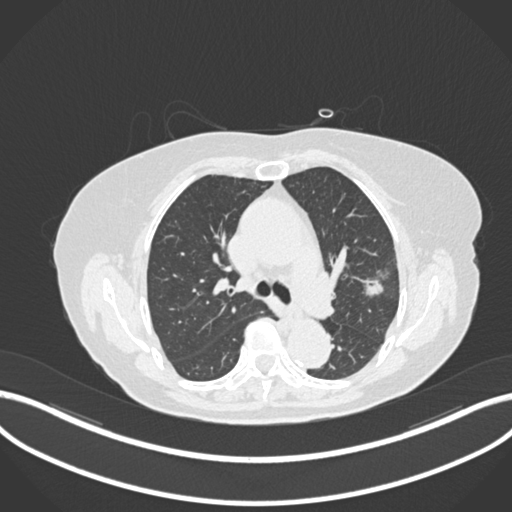
Chest CT, one axial slice. Slice 105 of 168 in the series (ordered by position). 120 kVp. Lung window (W 1500 / L -600 HU). 512 × 512 image matrix, field of view 400 × 400 mm. Patient: female, 75 years. Case-level facts recorded for this patient, not image findings: clinical TNM (as recorded): T1c N0 M0.
Outlined on this slice (rectangle marked by the reading radiologist):
- lung tumour (recorded histology: adenocarcinoma): bounding box (x1, y1, x2, y2) in pixels: (361, 272, 388, 301)